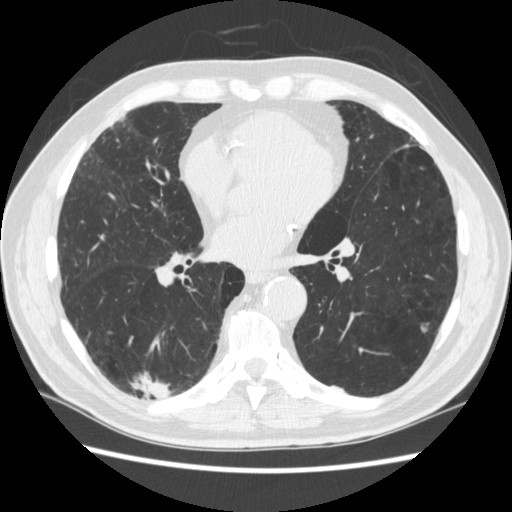
Axial slice from a low-dose chest CT screening exam; third annual screen; lung window (W 1500 / L -600 HU); slice 146 of 266 in the series; 512 × 512 image matrix, field of view 360 × 360 mm. Male participant, aged 70 years at enrolment.
Expert reader's lesion annotation, box from (x=123, y=361) to (x=184, y=420) px. The screening reader recorded 4 non-calcified nodules or masses ≥4 mm on this exam (right lower lobe, right lower lobe, left lower lobe, left lower lobe); which of them this box marks is not recorded. Later outcome: lung cancer diagnosed 253 days after this screen — squamous cell carcinoma, NOS, right upper lobe, poorly differentiated (G3), stage IV (AJCC 6th edition).